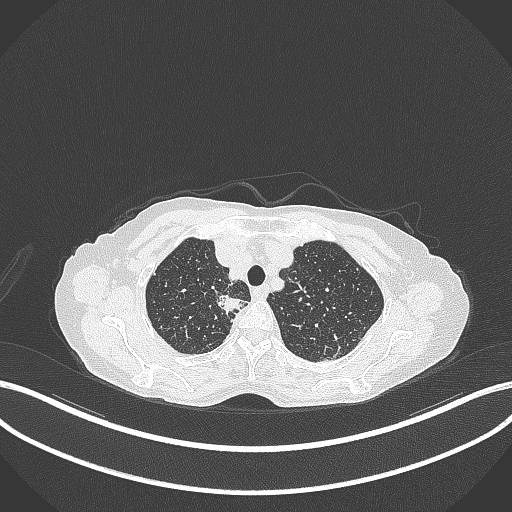
Chest CT, one axial slice; slice 310 of 403 in the series (ordered by position); reconstruction kernel B70f; 120 kVp; lung window (W 1500 / L -600 HU); 1 mm slice thickness; 512 × 512 image matrix, field of view 400 × 400 mm. Patient: female, 75 years. Case-level facts recorded for this patient, not image findings: clinical TNM (as recorded): T1c N1 M1.
Annotated regions visible in this slice (bounding box drawn by a radiologist):
- lung tumour (recorded histology: adenocarcinoma): bounding box [x1, y1, x2, y2] px = [213, 289, 248, 316]